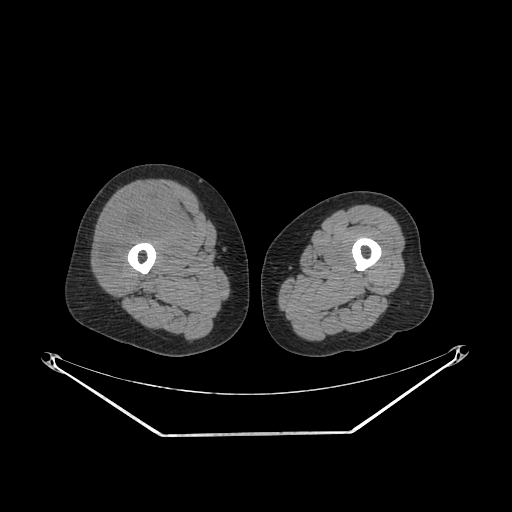
CT of an extremity soft-tissue mass (from a PET/CT study), one axial slice; position 236 of 311 along the scan axis; reconstruction kernel SOFT; soft-tissue window (W 400 / L 40 HU); 3.75 mm slice thickness; 512 × 512 image matrix, field of view 500 × 500 mm. Female patient. Case-level facts recorded for this patient, not image findings: histological type: pleiomorphic undifferentiated sarcoma; grade: high; site of the primary tumour: right quadricep.
Outlined on this slice (expert contour drawn on MRI and transferred to this co-registered scan by the dataset authors):
- tumour plus oedema (research contour): bounding box (x1, y1, x2, y2) in pixels: (100, 194, 184, 280)
- tumour (research contour): (100, 194, 184, 280)